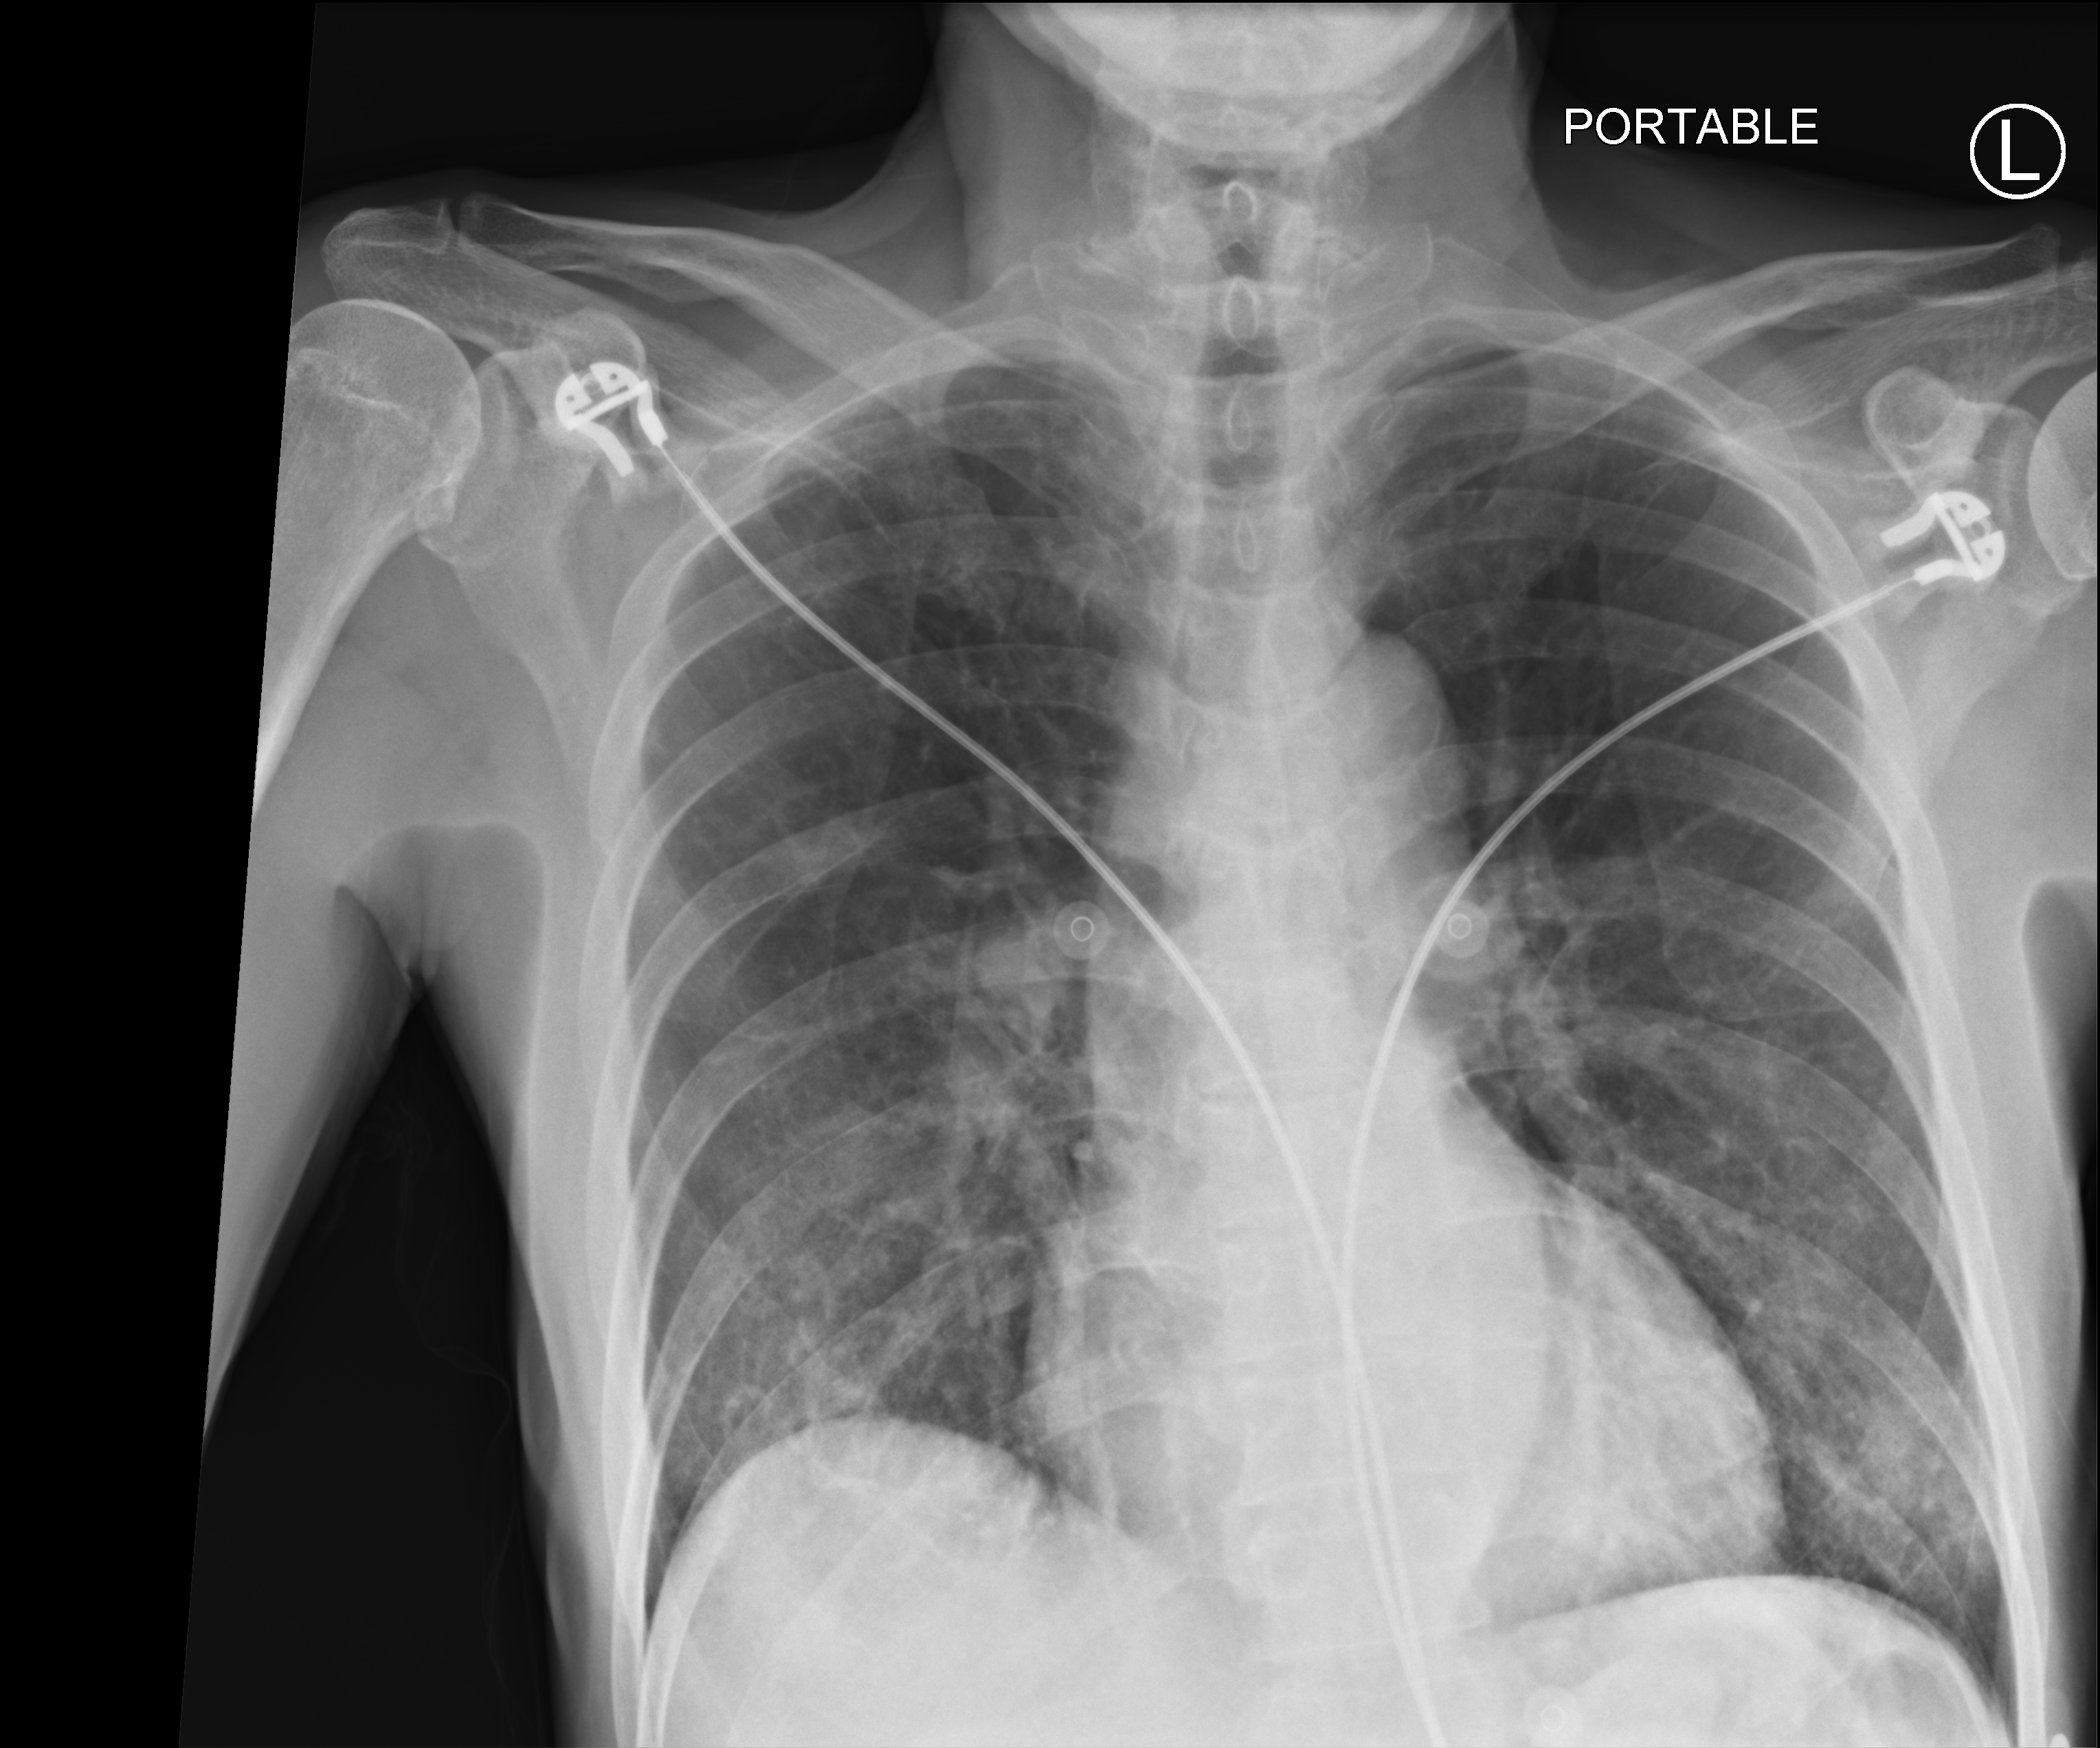
Chest X-ray (portable). Patient hospitalised with COVID-19; male, aged 60–74 years.
Hospital-stay facts (about this admission, not read from this image; timing relative to this image not recorded):
- admitted to intensive care during this hospital stay: no